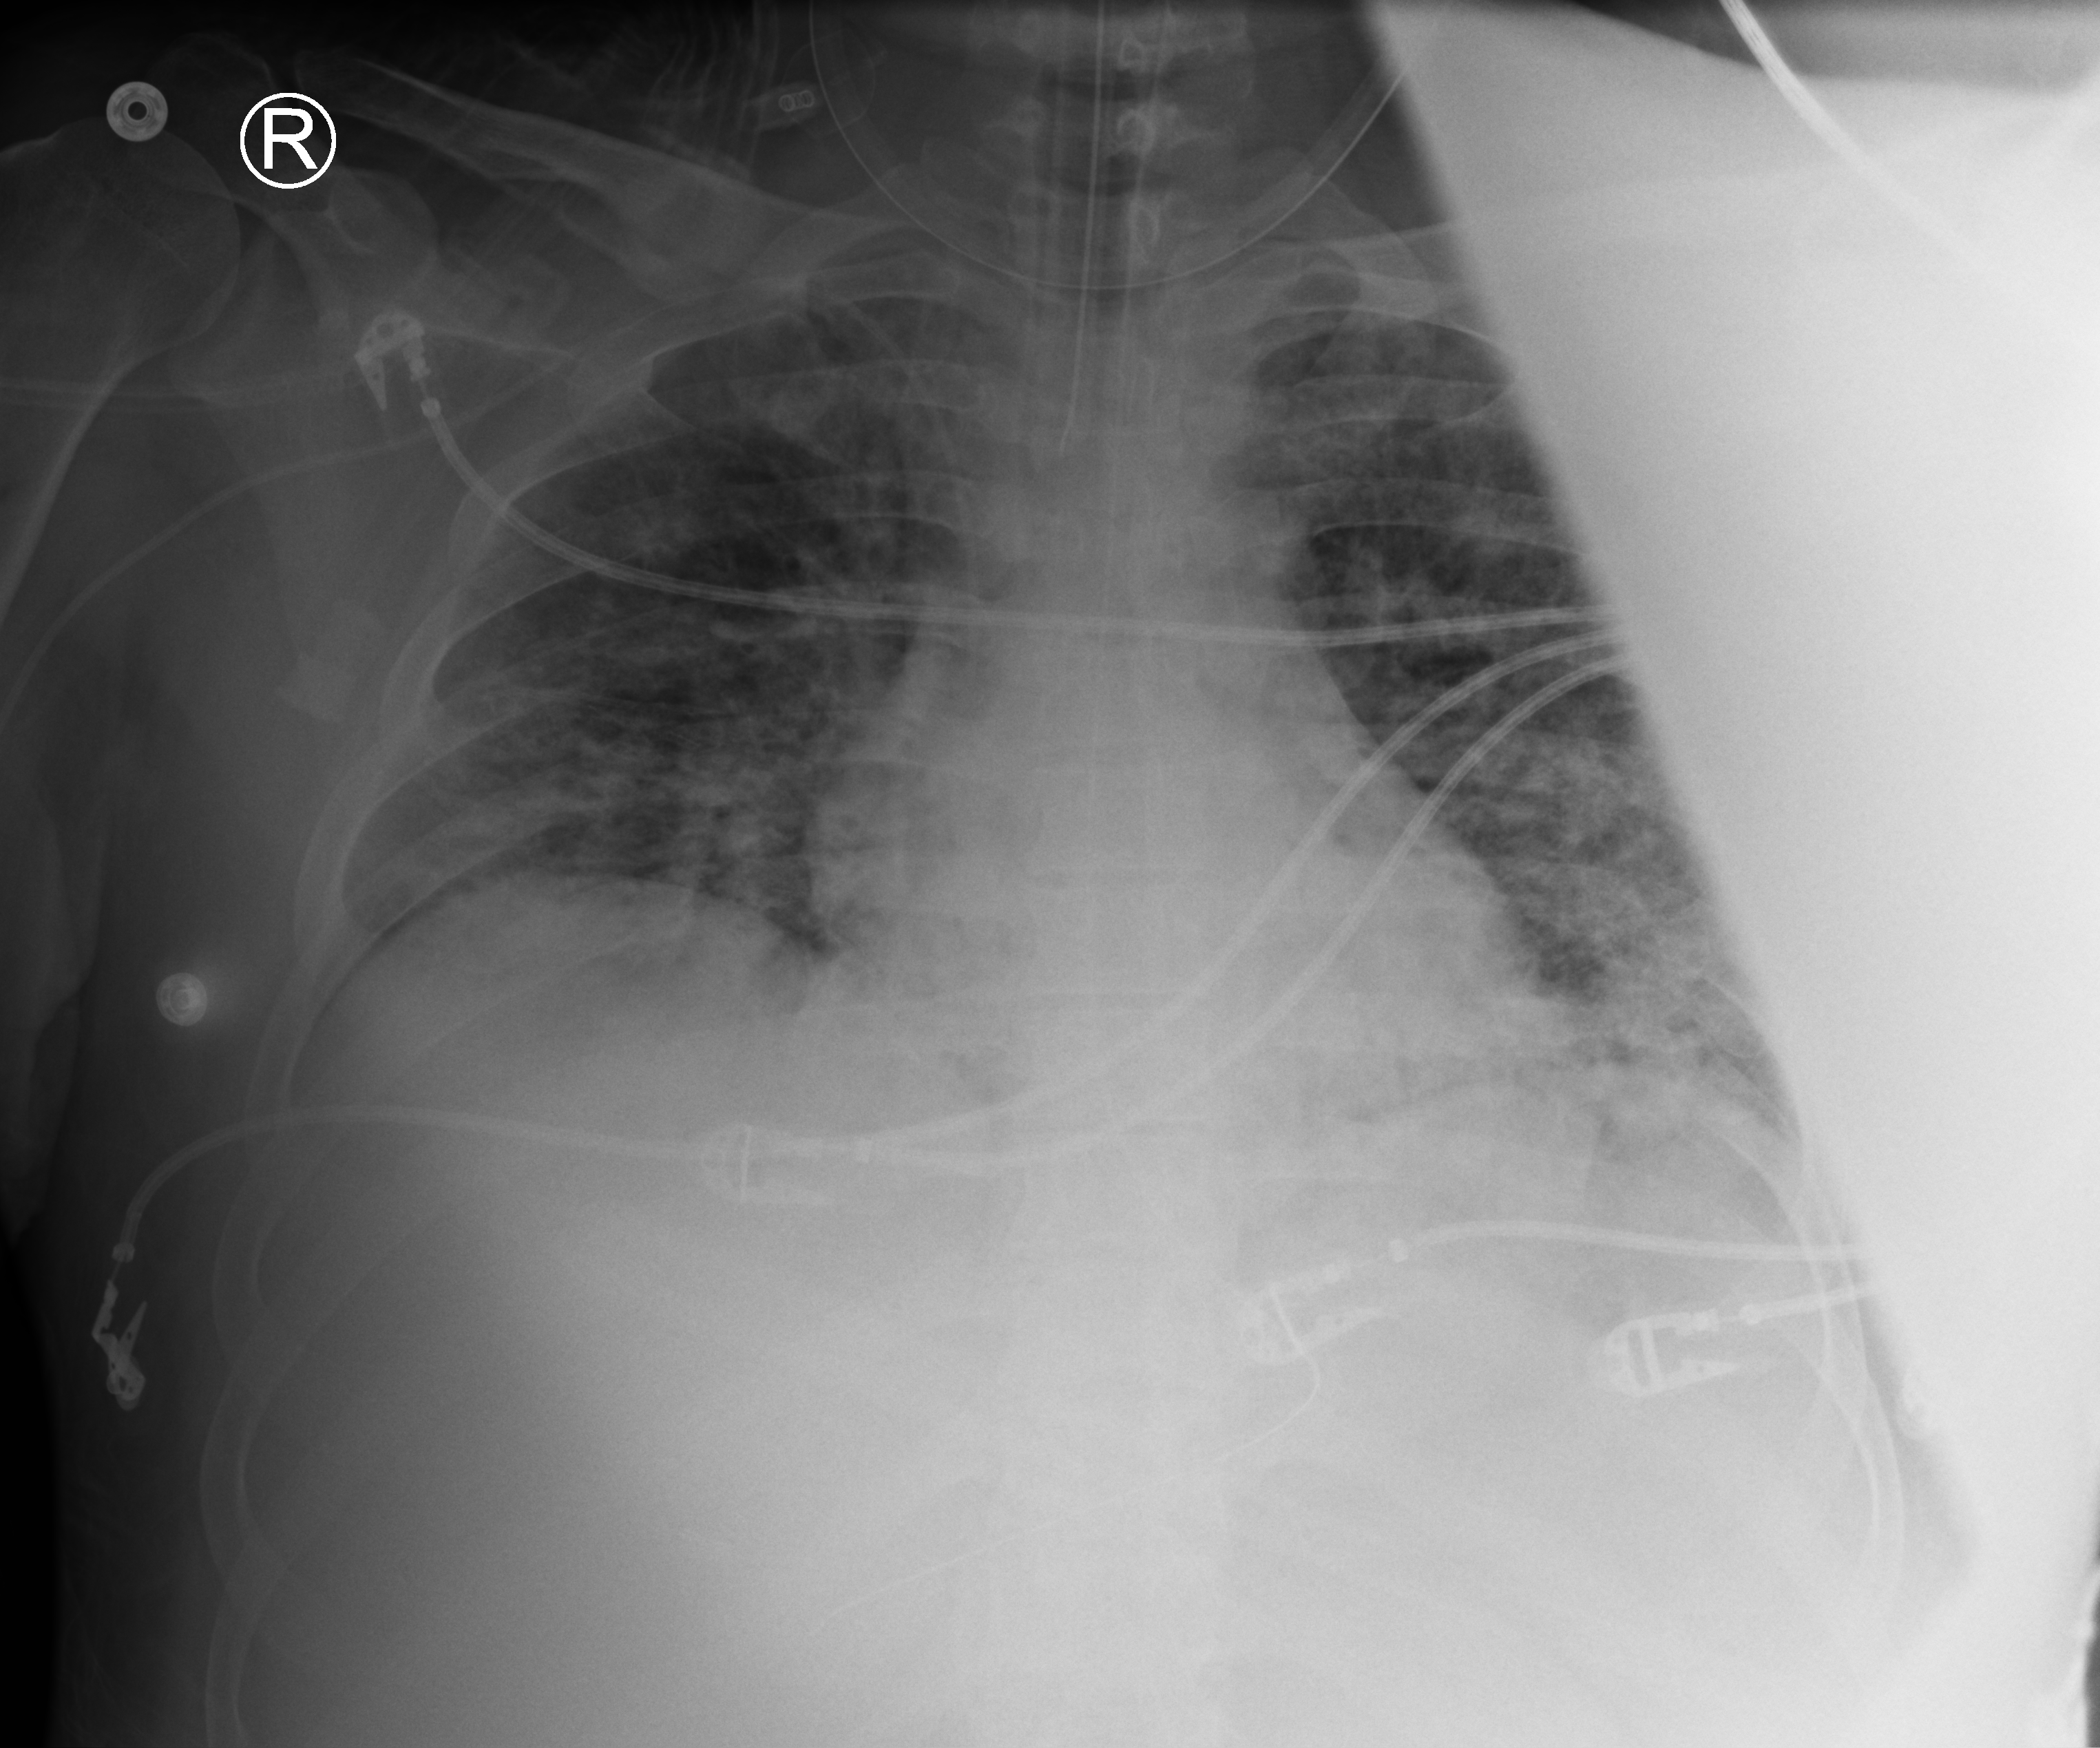
Bedside chest radiograph (computed radiography), anteroposterior (AP) projection. Patient hospitalised with COVID-19; male, aged 18–59 years.
Hospital-stay facts (about this admission, not read from this image; timing relative to this image not recorded):
- smoking status (admission record): former
- mechanically ventilated during this hospital stay: yes
- admitted to intensive care during this hospital stay: yes